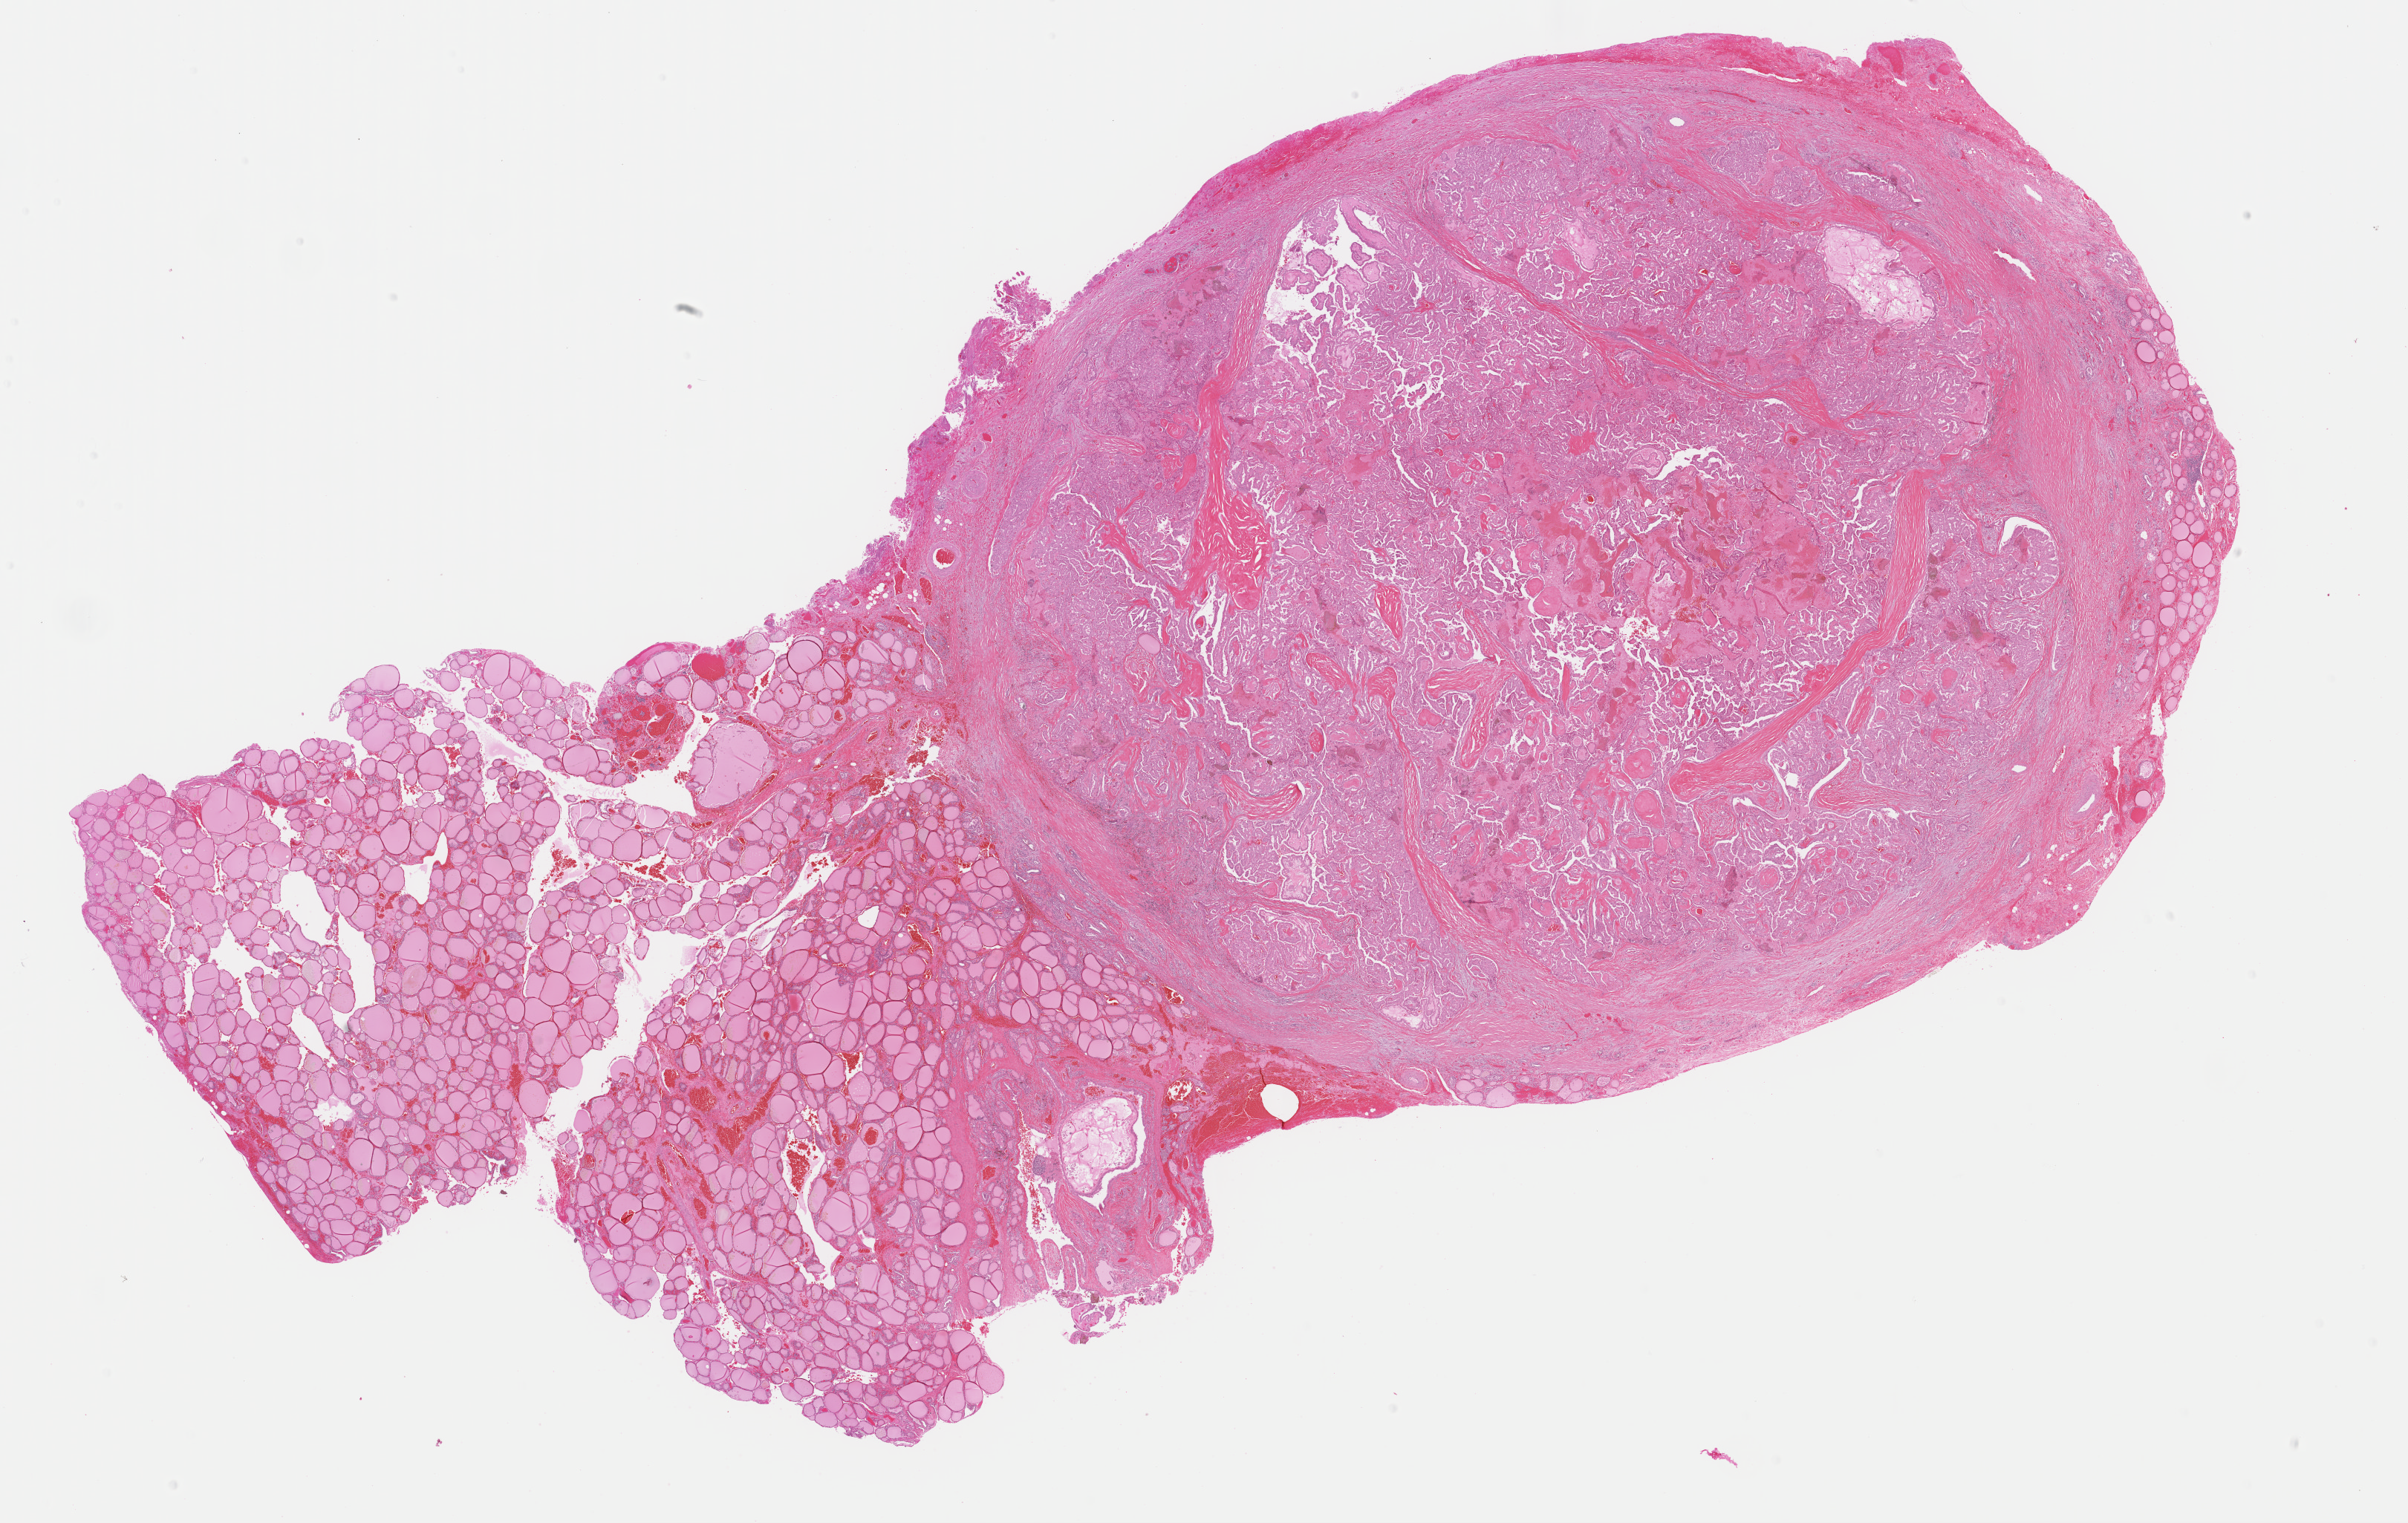
Whole-slide histology image, Hematoxylin and eosin (H&E) stained, a low-resolution overview of the entire scanned area, about 25.6 x 16.2 mm (from a 40x scan), formalin-fixed paraffin-embedded (FFPE) diagnostic section, sample: primary tumour, thyroid. Patient: female, age at initial diagnosis 42 years.
• diagnosis: Papillary adenocarcinoma, NOS (thyroid gland)
• AJCC pathologic stage: I (6th edition)